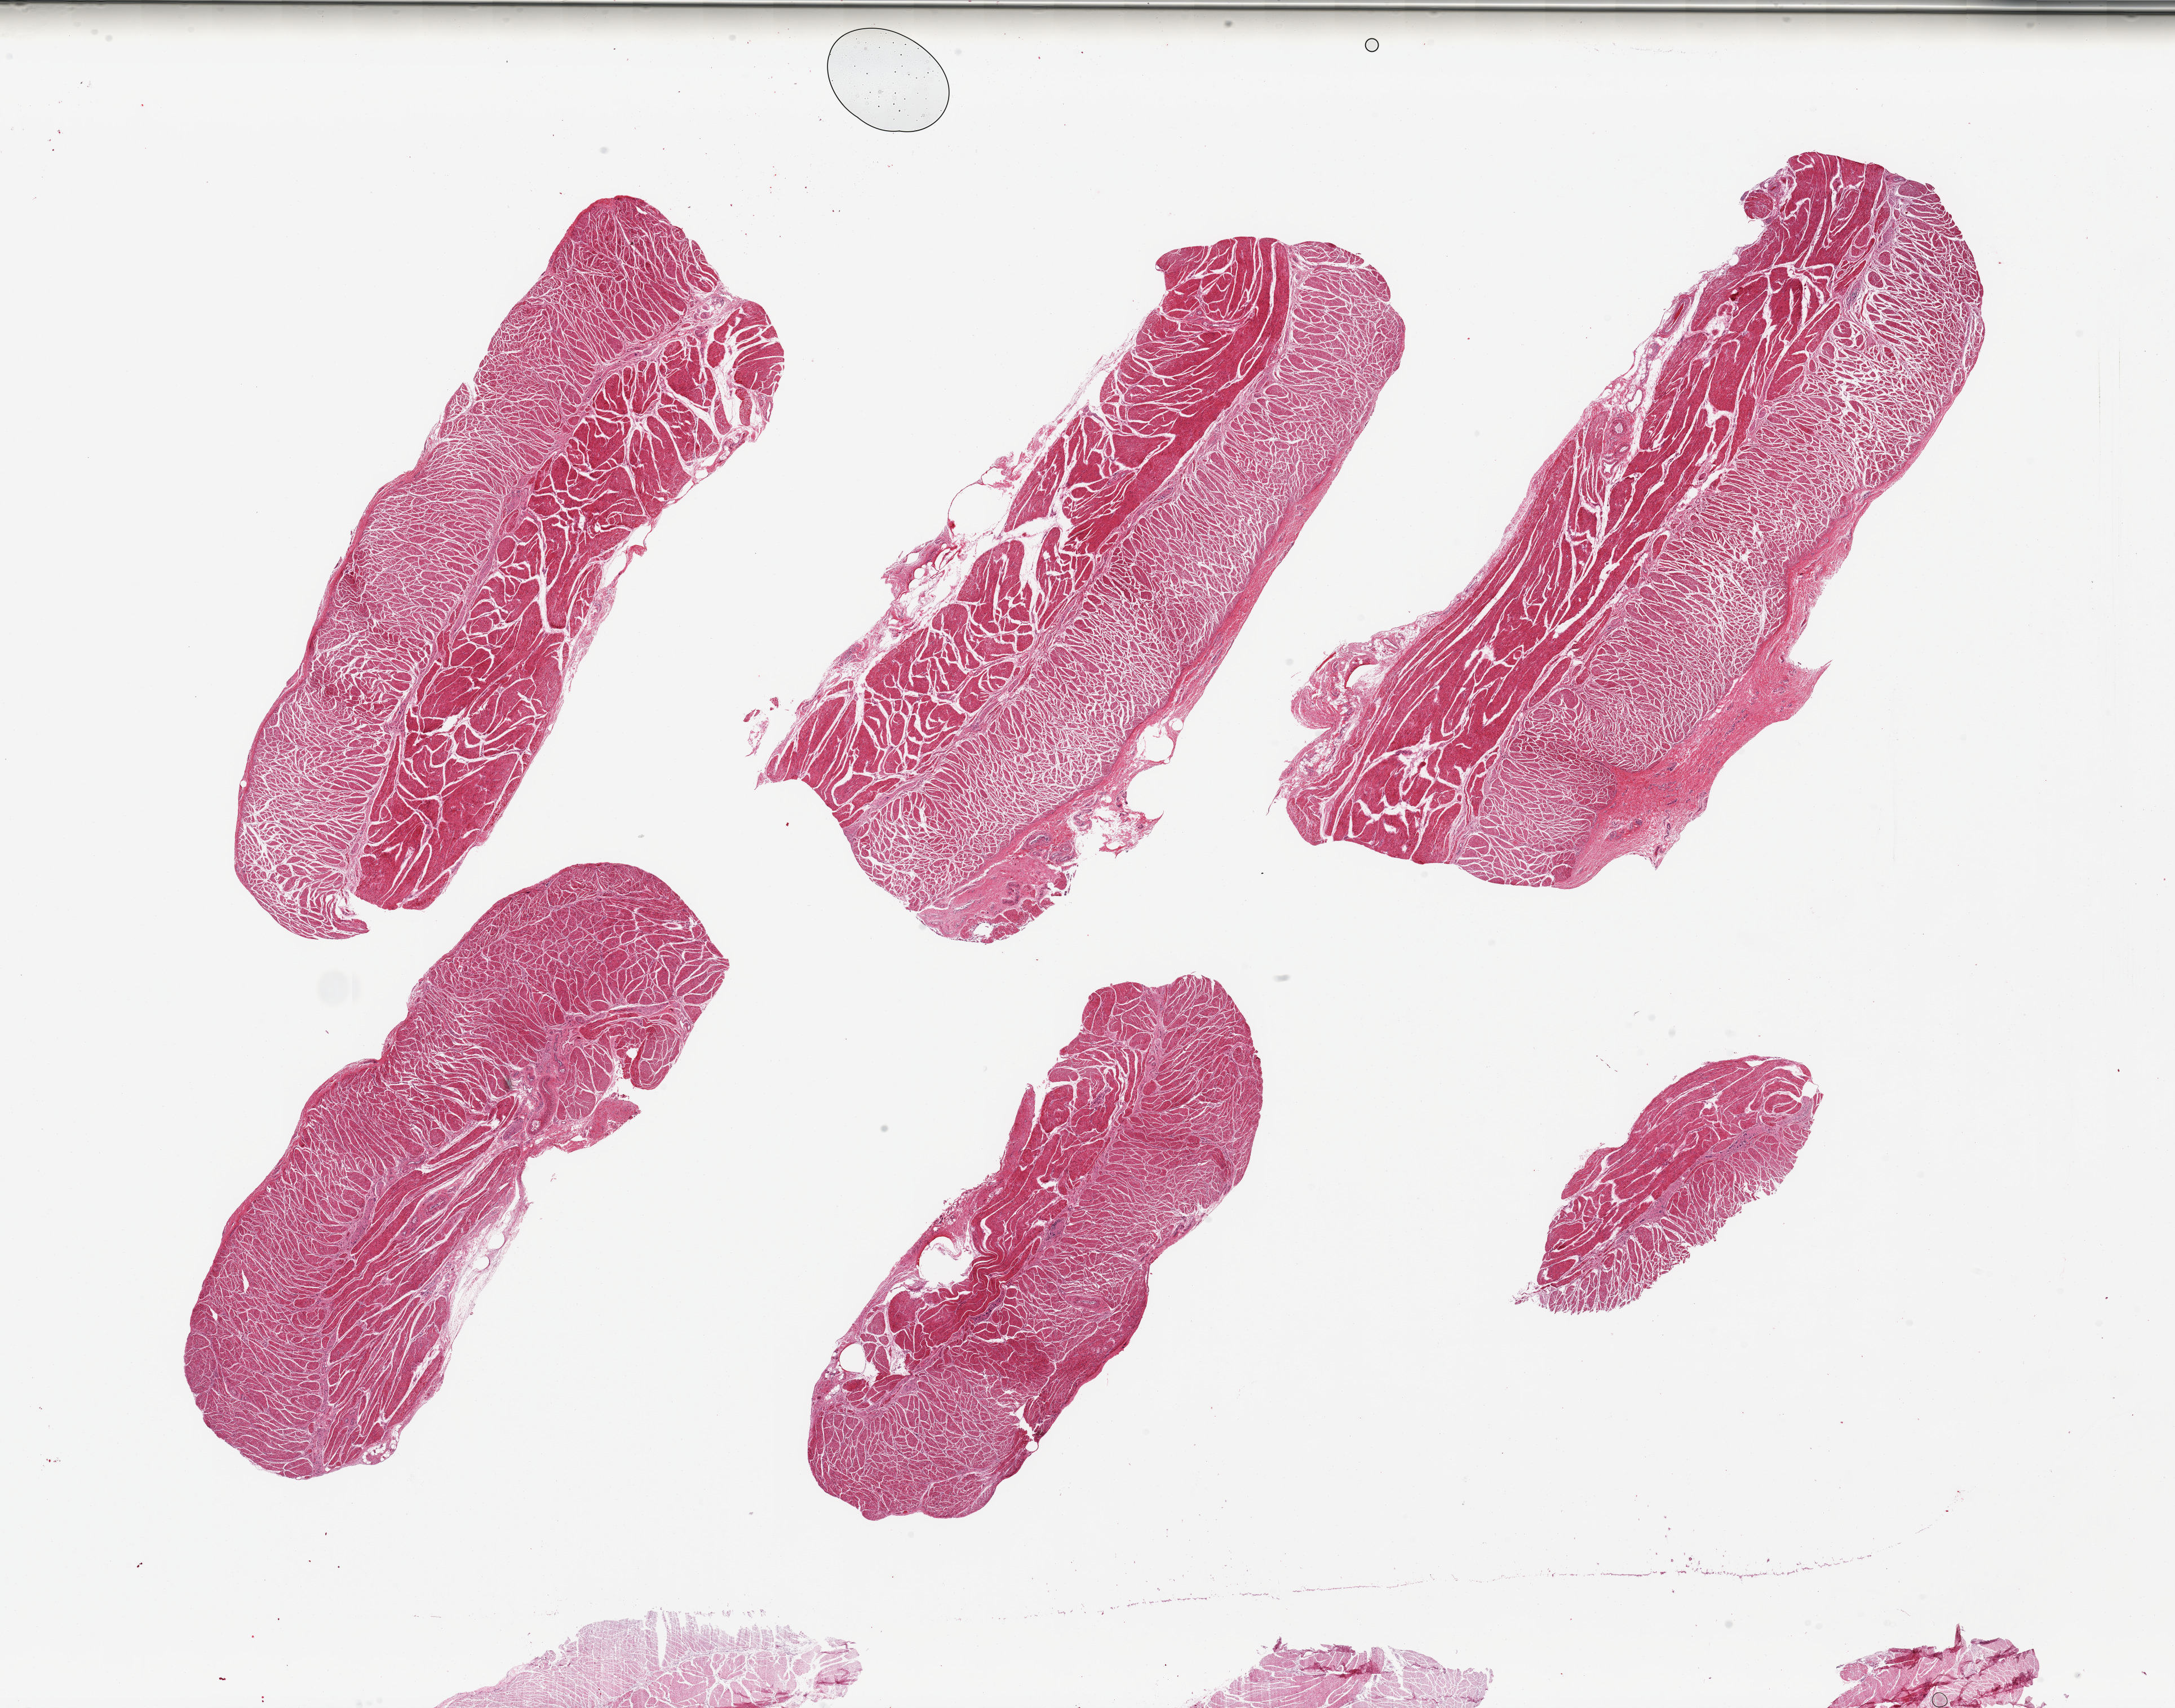
Whole-slide image, haematoxylin and eosin stain, brightfield — shown as a low-resolution overview of the whole scanned area (about 30.5 x 24.0 mm), PAXgene-fixed paraffin-embedded (PFPE) section, target tissue: gastroesophageal junction, donor tissue sample. Donor: male.
• reviewer comment on this tissue sample: 6 muscular pieces, 5 large, 1 small, plus 3 small nonmuscular fragments